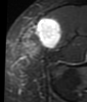
MRI of an extremity soft-tissue mass, one axial slice; STIR; MR volume resampled by the dataset authors to the PET/CT grid (not the native acquisition matrix); 87 × 102 image matrix, field of view 85 × 100 mm. Female patient. Case-level facts recorded for this patient, not image findings: histological type: synovial sarcoma; grade: intermediate; site of the primary tumour: right thigh.
Outlined on this slice (expert contour drawn on MRI and transferred to this co-registered scan by the dataset authors):
- gross tumour volume including surrounding oedema: bounding box [x1, y1, x2, y2] px = [26, 18, 62, 53]
- gross tumour volume (mass): [26, 18, 62, 55]